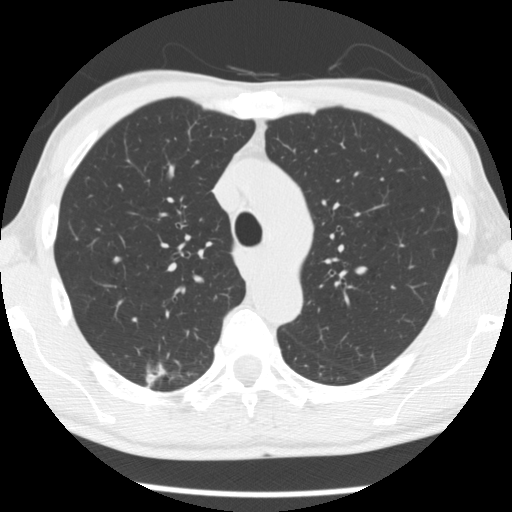
Chest CT (low-dose screening protocol), one axial image, baseline screening round, lung window (W 1500 / L -600 HU), 2.5 mm slice thickness, standard (soft-tissue) reconstruction kernel (STANDARD). Male participant, aged 66 years at enrolment.
- Lesion marked by an expert reader, bounding box <134,356,188,398> (left, top, right, bottom; pixels).
- The screening reader recorded 4 non-calcified nodules or masses ≥4 mm on this exam; which of them this box marks is not recorded.
- Later outcome: lung cancer diagnosed 503 days after this screen — adenocarcinoma, NOS, right upper lobe, undifferentiated (G4), stage IA (AJCC 6th edition), 20 mm at pathology.